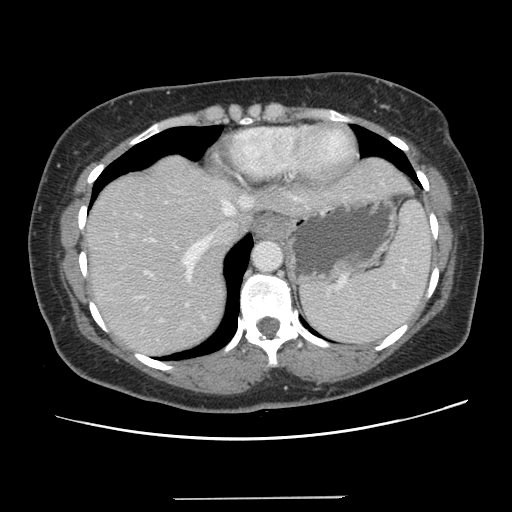
Contrast-enhanced abdominal CT, one axial slice; slice 110 of 141 in the series (ordered by position); 120 kVp; intravenous contrast given; soft-tissue window (W 400 / L 40 HU); 2.5 mm slice thickness; 512 × 512 image matrix, field of view 366 × 366 mm. Female patient, age 53 years. From the clinical record (not read from this slice): diagnosis: colorectal cancer liver metastases, imaged before liver resection; multiple liver metastases: no; largest metastasis: 14.5 cm; disease in both lobes: yes.
Annotated regions visible in this slice (manually delineated by an expert):
- hepatic veins: bounding box (x1, y1, x2, y2) in pixels: (113, 195, 304, 281)
- liver: (86, 155, 410, 357)
- planned liver remnant (the part of the liver to remain after resection): (85, 208, 254, 357)
- portal vein (with intrahepatic branches): (139, 202, 189, 322)